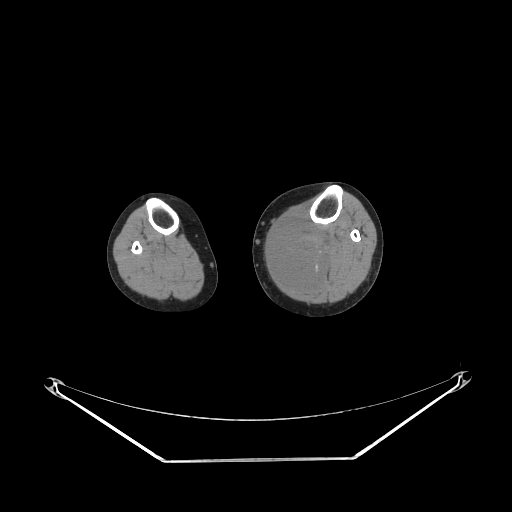
CT of an extremity soft-tissue mass (from a PET/CT study), one axial slice. Position 146 of 223 along the scan axis. 140 kVp. Soft-tissue window (W 400 / L 40 HU). 512 × 512 image matrix, field of view 500 × 500 mm. Female patient. From the clinical record (not read from this slice): histological type: extraskeletal high grade osteogenic sarcoma; grade: high; site of the primary tumour: left calf.
Structures marked on this image (expert contour drawn on MRI and transferred to this co-registered scan by the dataset authors):
- gross tumour volume (mass): bounding box <270,219,330,286> (left, top, right, bottom; pixels)